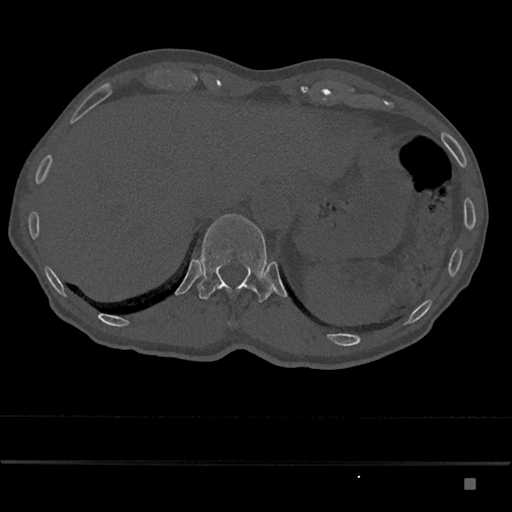
CT including the spine, one axial slice. Position 624 of 797 along the scan axis. 120 kVp. Bone window (W 1800 / L 400 HU). 512 × 512 image matrix, field of view 390 × 390 mm. Patient: male, 72 years. Case-level facts recorded for this patient, not image findings: primary cancer: prostate.
Annotated regions visible in this slice (semi-automatically segmented with operator editing):
- T11 vertebra: box from (x=228, y=323) to (x=230, y=325) px
- T12 vertebra: (x=197, y=214)–(x=274, y=303)